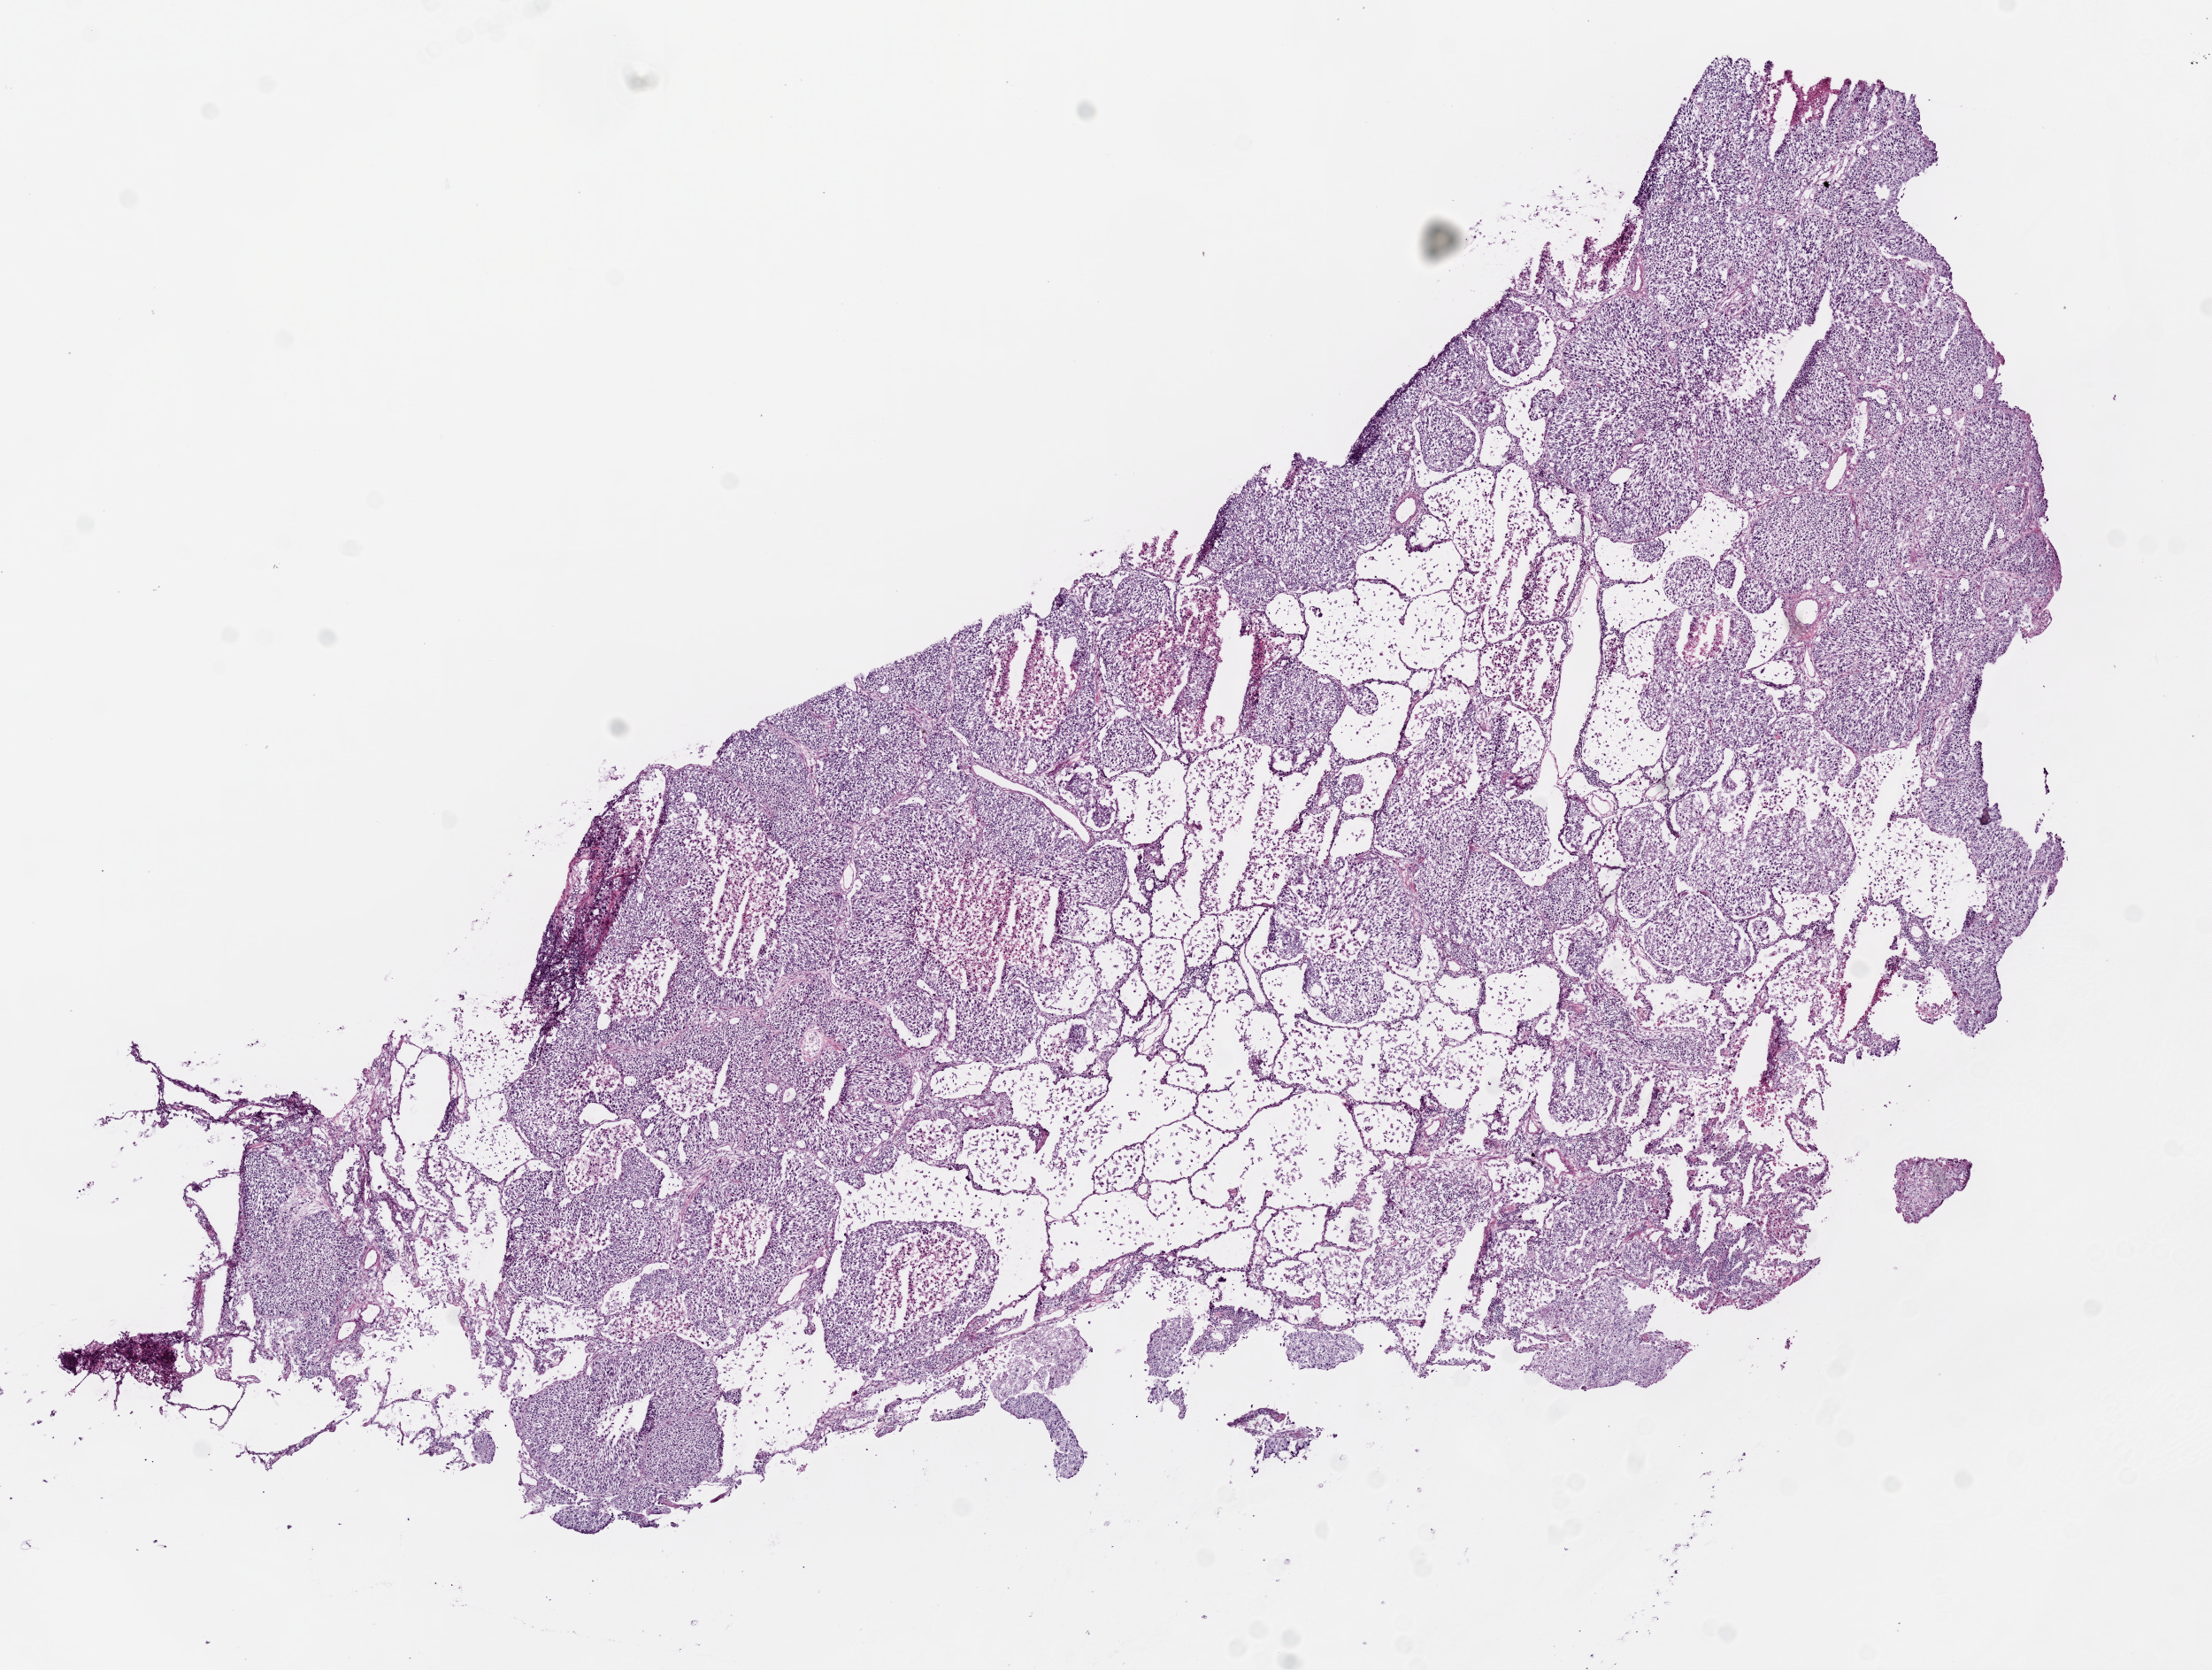
Whole-slide histology image, H&E-stained — low-resolution overview of the scanned area, about 10.0 x 7.6 mm (slide scanned at 20x). Frozen section. Sample: primary tumour, lung. Patient: male, age at initial diagnosis 80 years. Slide review estimates, as recorded: tumour cells 75%, tumour nuclei 80%, normal cells 20%, stromal cells 5%, necrosis 0%.
Laterality: right. Diagnosis: Squamous cell carcinoma, NOS (lower lobe, lung). AJCC pathologic stage: IIIA.